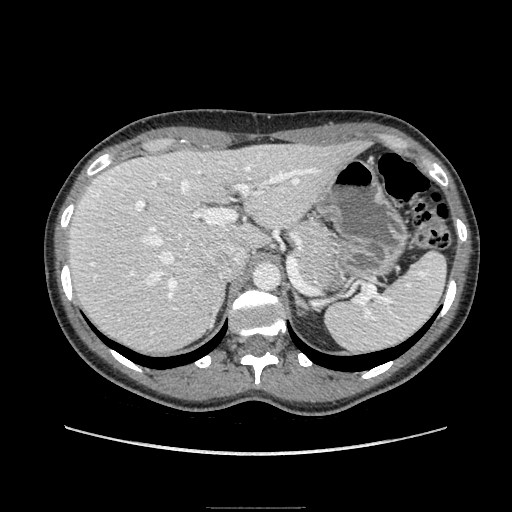
Contrast-enhanced abdominal CT, one axial slice. Position 127 of 193 along the scan axis. Soft-tissue window (W 400 / L 40 HU). 512 × 512 image matrix, field of view 380 × 380 mm. Female patient. Case-level facts recorded for this patient, not image findings: diagnosis: adrenocortical carcinoma; tumour side: right adrenal; tumour size at pathology: 3 cm; Ki-67 index: 4 %; stage (as recorded): 1.
Structures marked on this image (semi-automatic segmentation, software-assisted and operator-edited):
- mass: bounding box (x1, y1, x2, y2) in pixels: (197, 277, 223, 322)